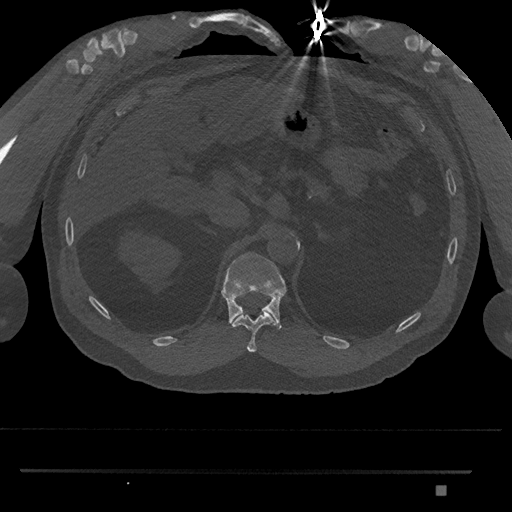
CT including the spine, one axial slice; slice 916 of 1134 in the series (ordered by position); 120 kVp; bone window (W 1800 / L 400 HU); 512 × 512 image matrix, field of view 429 × 429 mm. Patient: male, 65 years. Case-level facts recorded for this patient, not image findings: primary cancer: prostate.
Outlined on this slice (semi-automatically segmented with operator editing):
- T11 vertebra: box from (x=232, y=312) to (x=276, y=352) px
- T12 vertebra: (x=221, y=252)–(x=287, y=330)